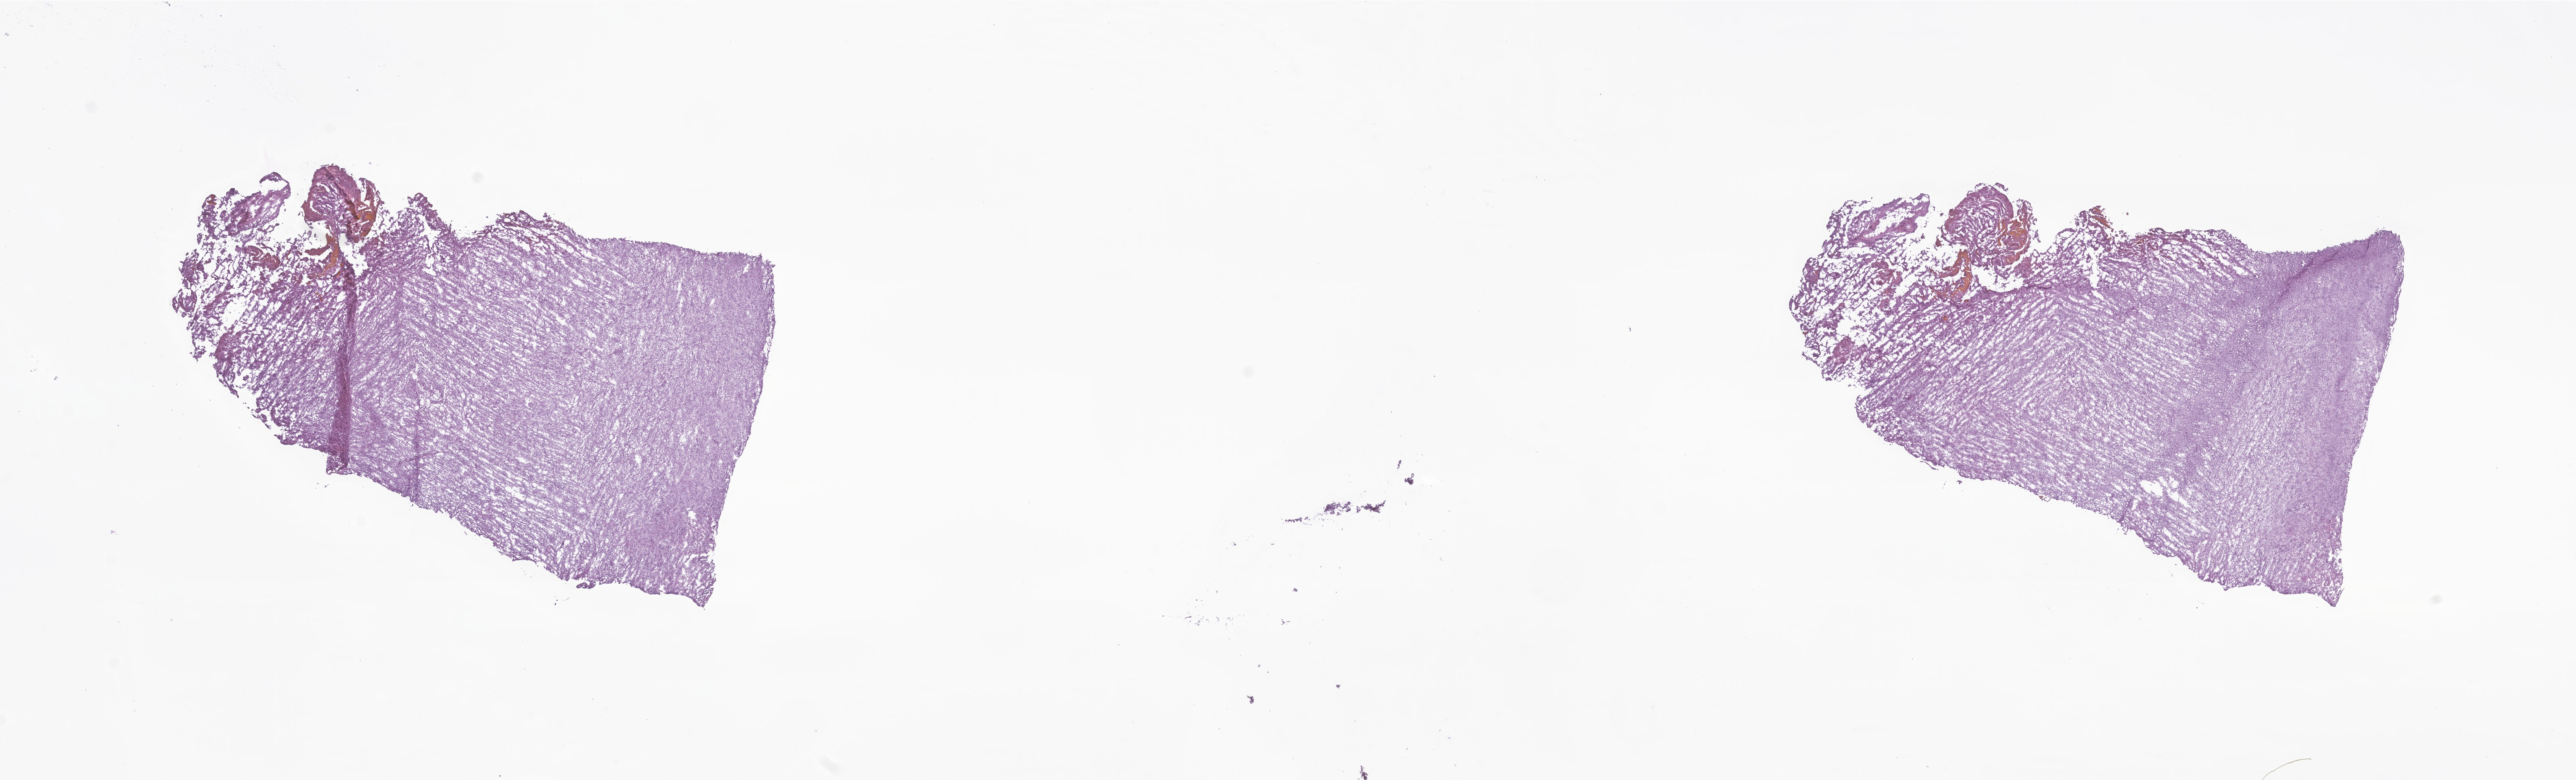
H&E whole-slide image of tumor tissue from the brain — whole scanned area (about 27.6 x 8.4 mm) shown as a low-resolution overview, frozen section (OCT-embedded). Patient female; age 88 months (7 years 4 months).
* recorded diagnosis: Meningioma, NOS